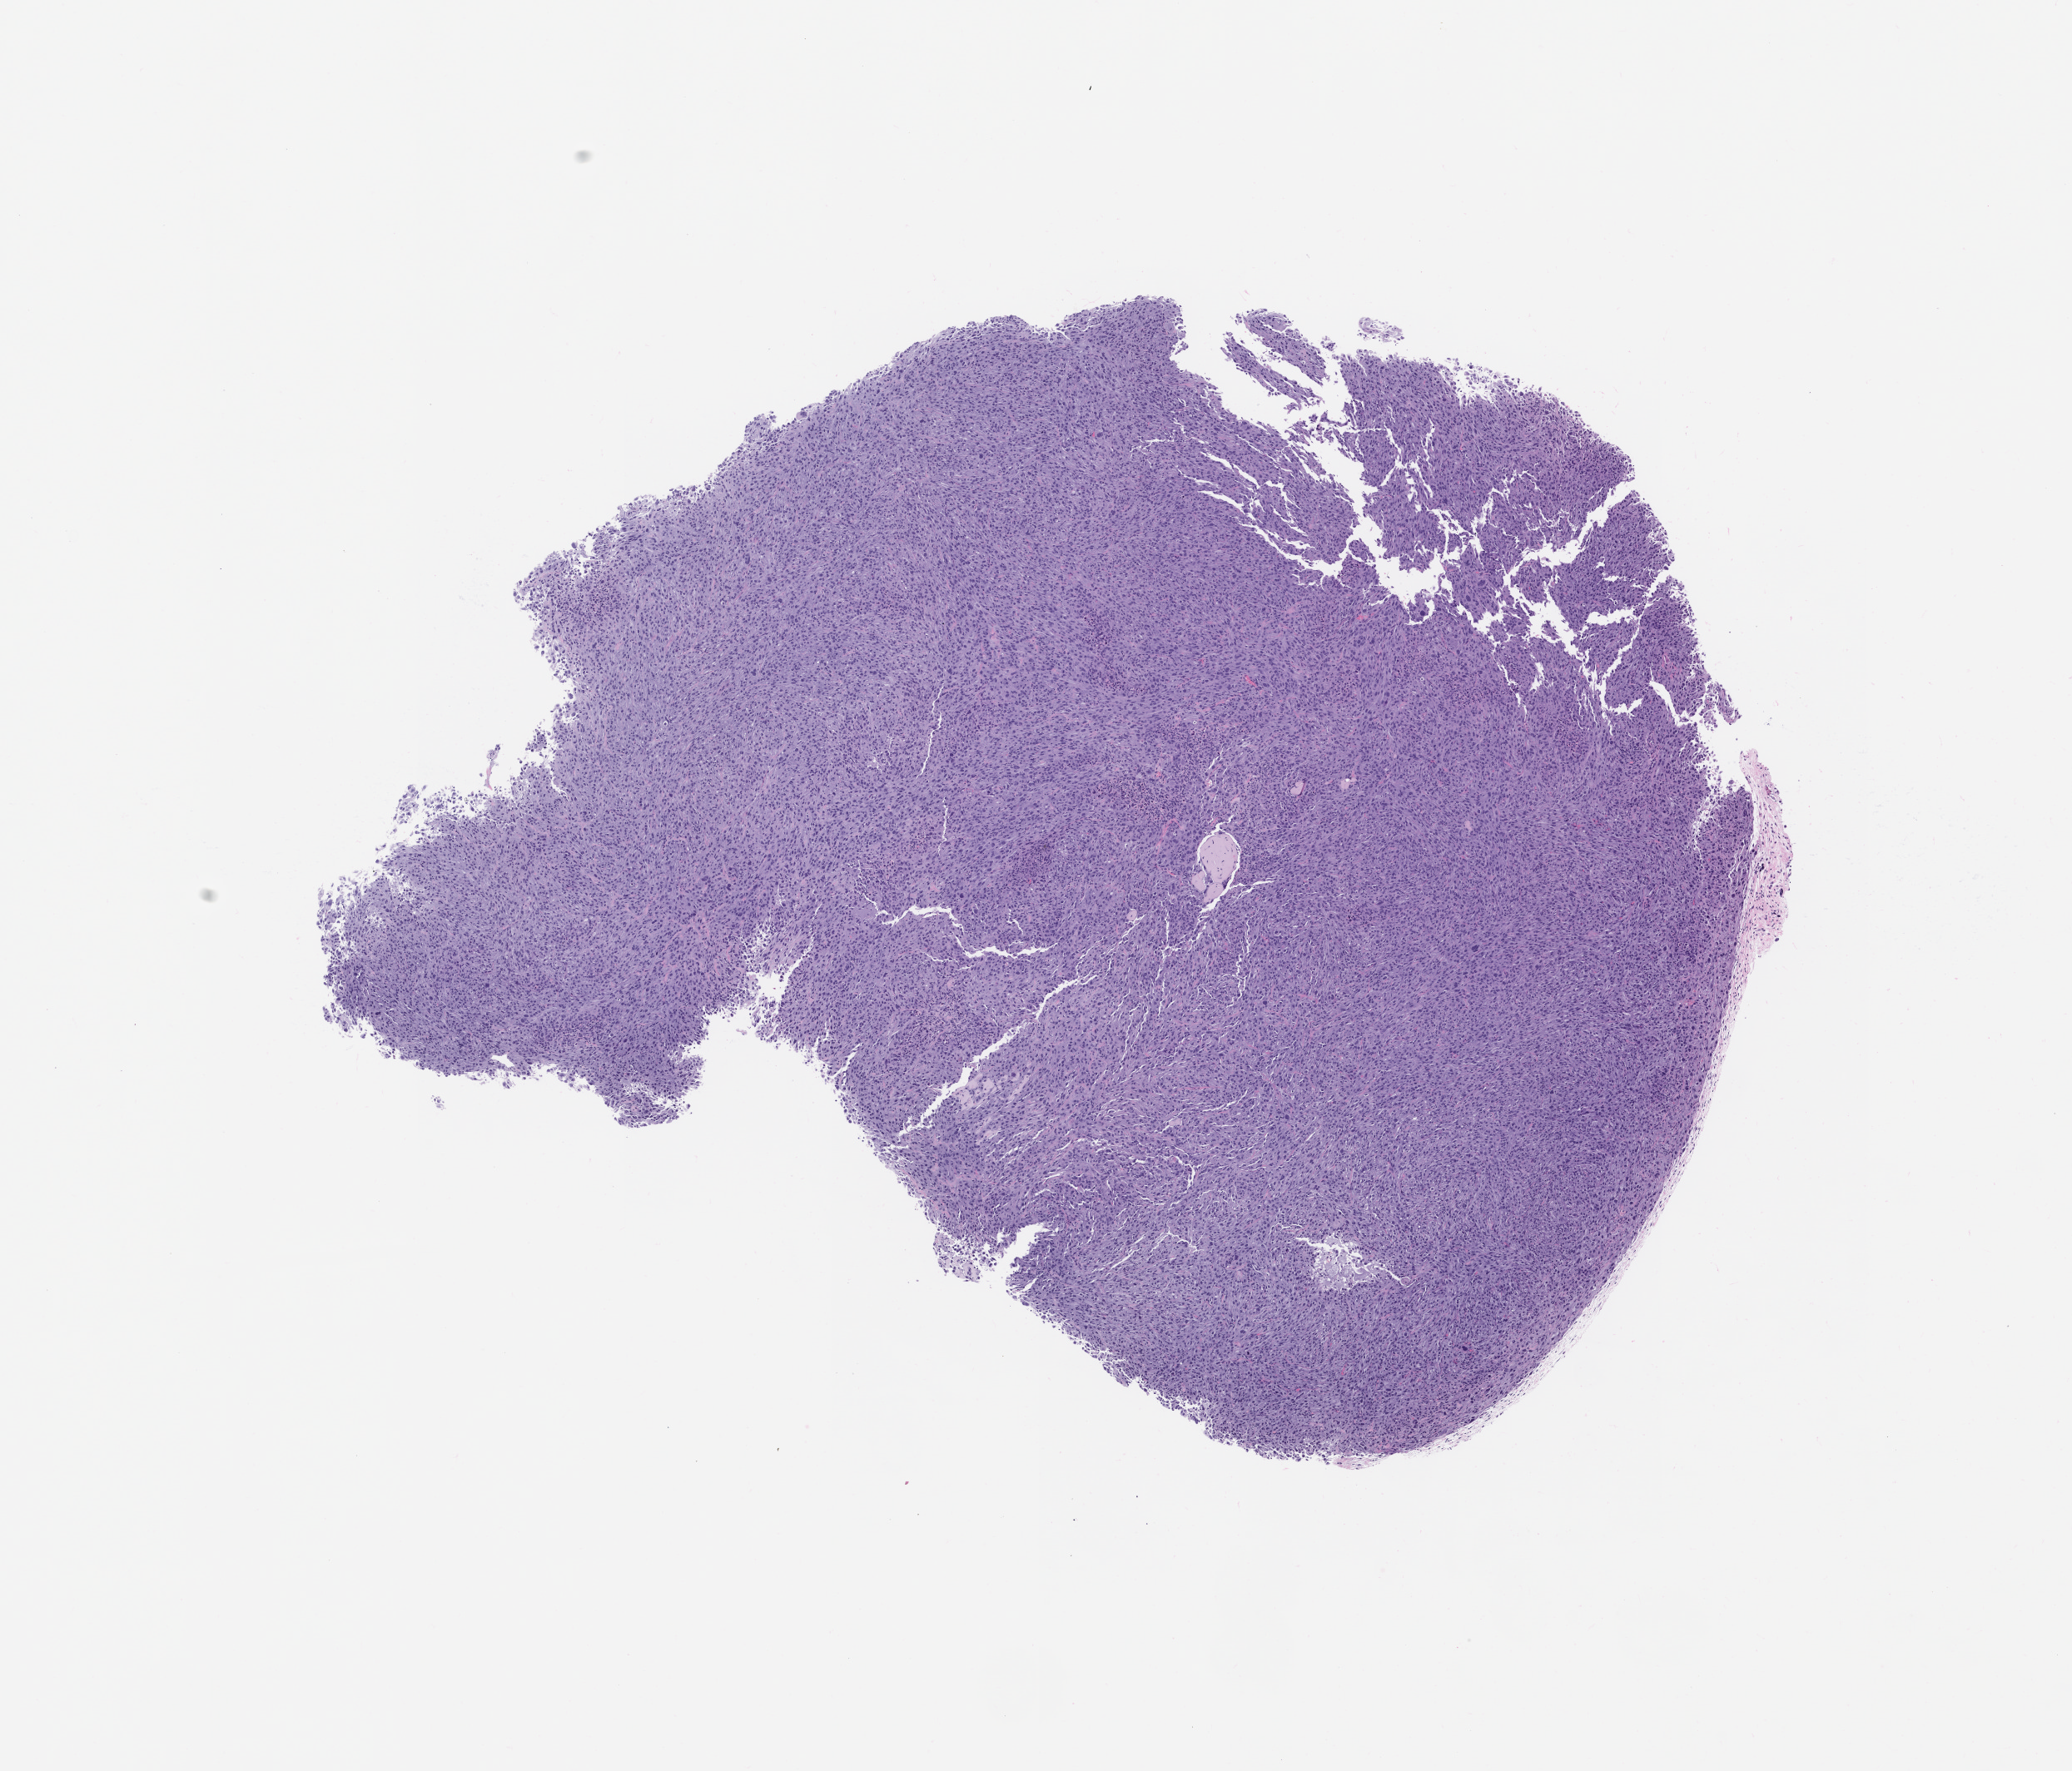
H&E whole-slide image of a patient-derived xenograft (PDX) tumor grown in a mouse, passage 0, a low-resolution overview of the entire scanned area, about 10.0 x 8.5 mm; formalin-fixed paraffin-embedded section; originating tumor site category: thyroid.
Originating patient diagnosis: Thyroid Gland Oncocytic Carcinoma.